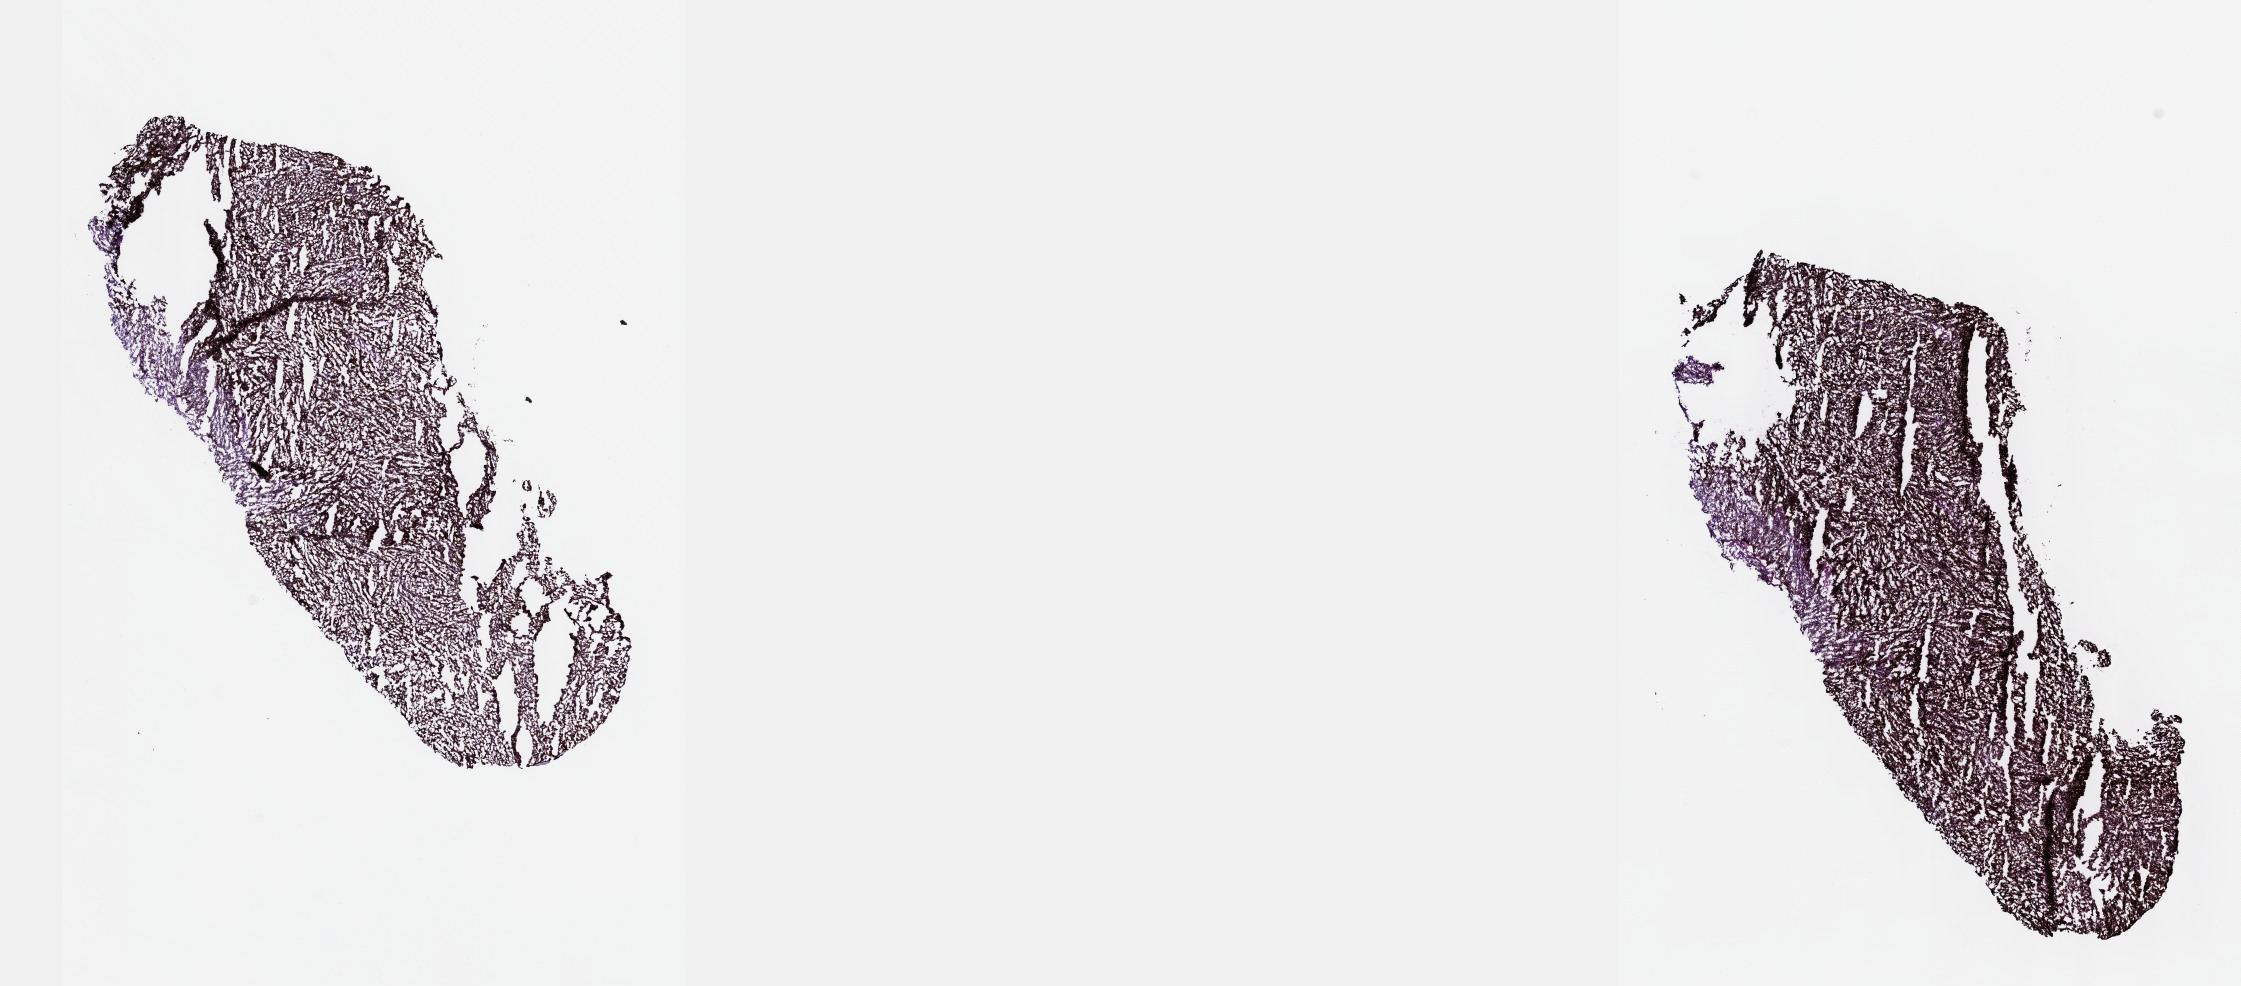
H&E-stained whole-slide image — low-resolution overview of the scanned area, about 18.1 x 8.0 mm (slide scanned at 40x). Frozen section from the top of the tissue portion. Uvea, primary tumour sample. Patient: male, age at initial diagnosis 71 years.
Diagnosis: Spindle cell melanoma, type B (choroid).